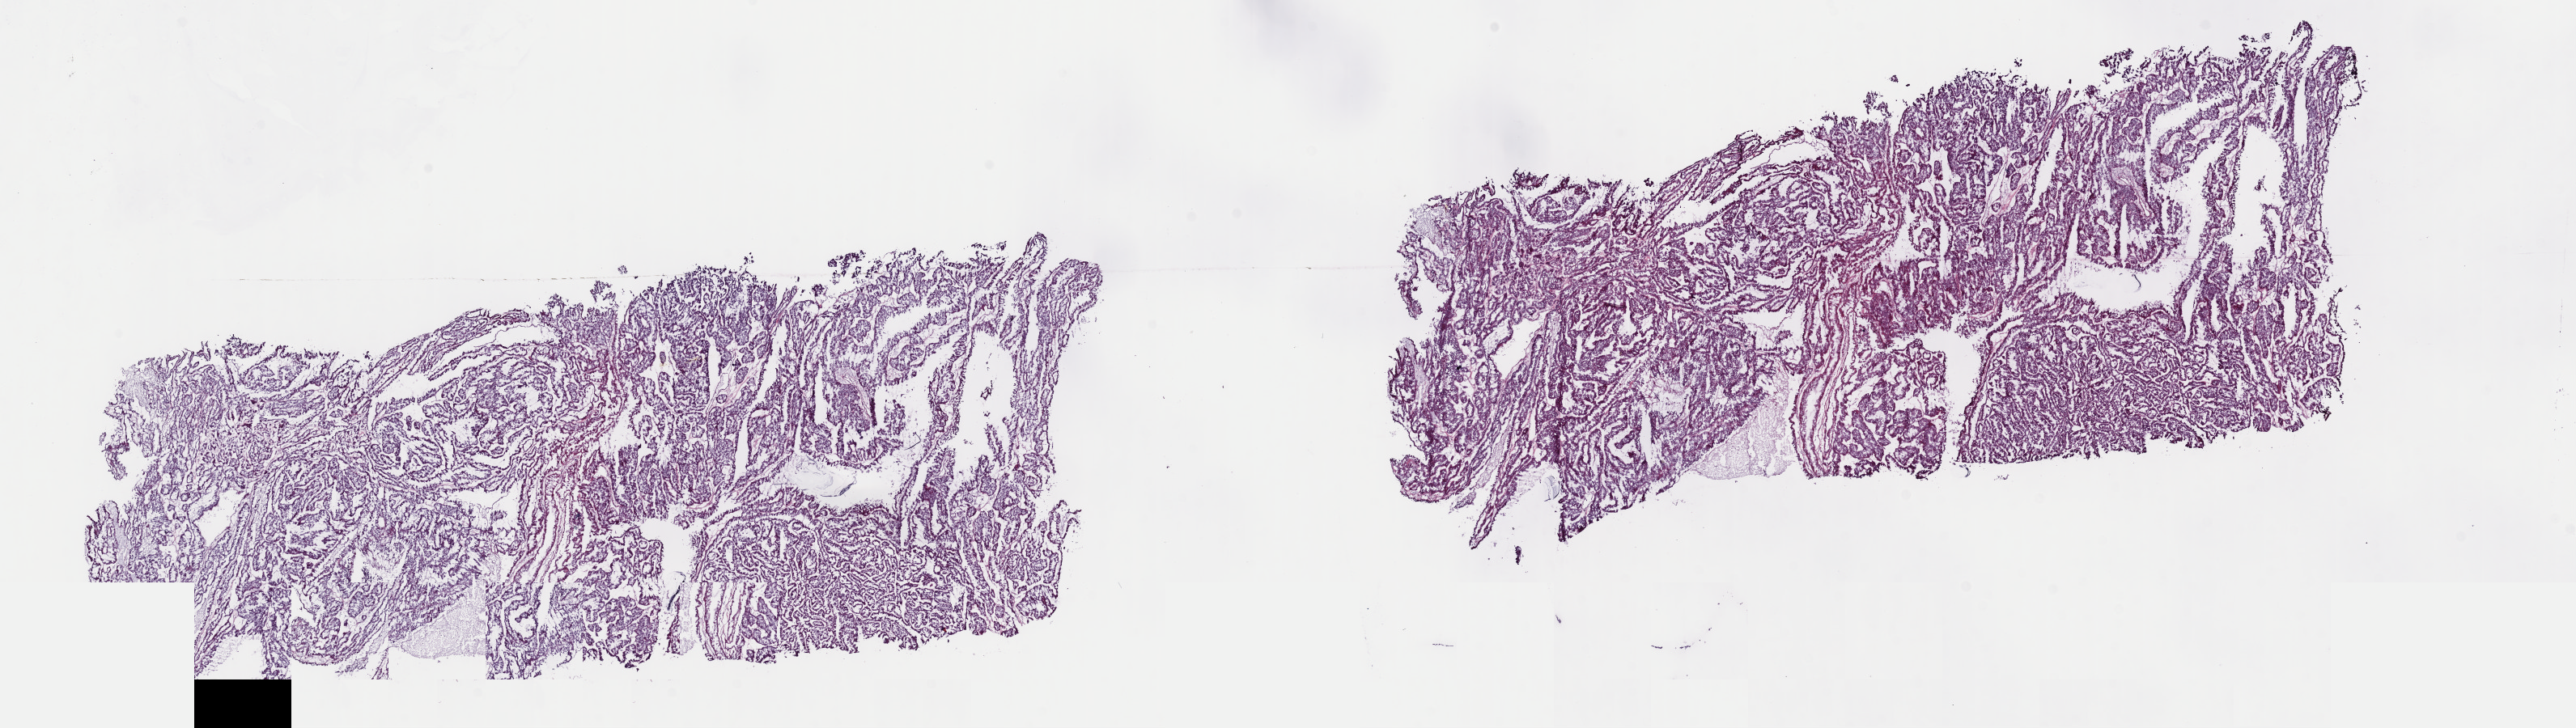
H&E-stained whole-slide image, low-resolution overview of the scanned area, about 25.1 x 7.1 mm (from a 40x scan). Frozen section. Primary tumour sample from the kidney. Female, age 61 years at initial diagnosis. Pathologist review of this section (percent, as recorded): tumour cells 90%, tumour nuclei 80%, normal cells 0%, stromal cells 0%, necrosis 10%. Inflammatory infiltration, as recorded: lymphocyte infiltration 1%, monocyte infiltration 3%, neutrophil infiltration 0%.
* laterality: left
* pathologic diagnosis: Papillary adenocarcinoma, NOS
* AJCC pathologic stage: I